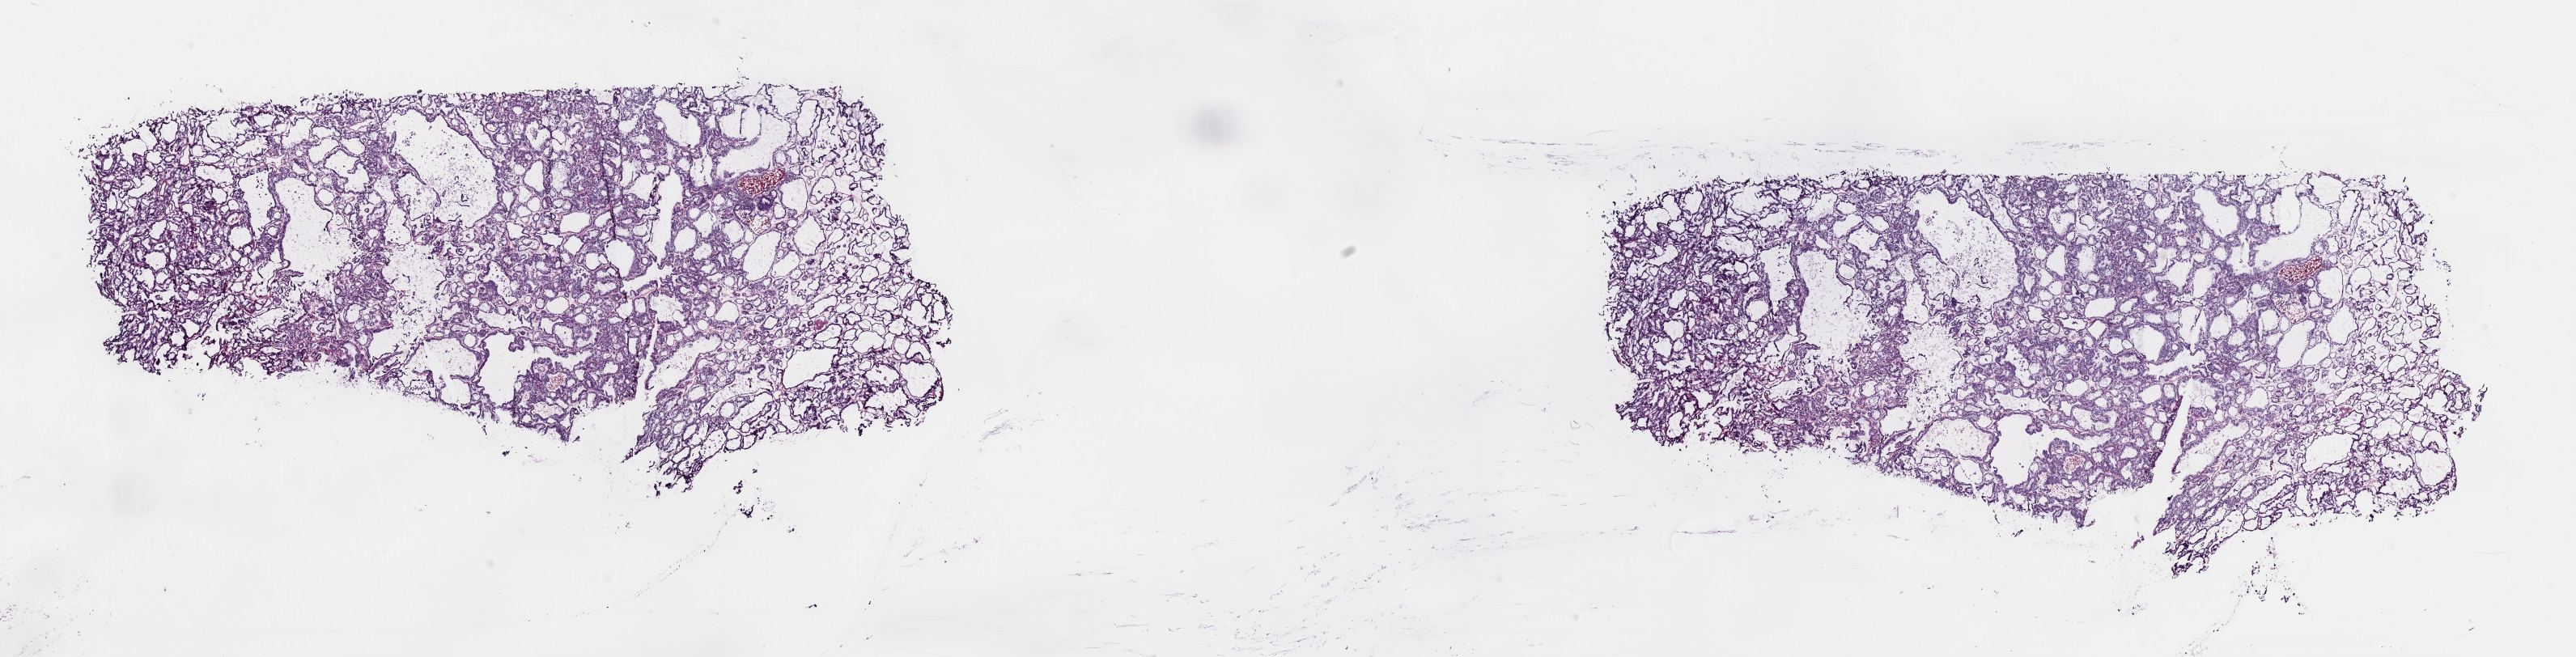
Whole-slide histology image, H&E — whole scanned area (about 25.1 x 6.4 mm, from a 40x scan) shown as a low-resolution overview. Frozen section. Primary tumour sample from the thyroid. Female patient; age at initial diagnosis 38 years. Composition of this section per pathologist review: tumour cells 75%, tumour nuclei 75%, normal cells 0%, stromal cells 21%, necrosis 4%. Inflammatory infiltration, as recorded: lymphocyte infiltration 4%, monocyte infiltration 1%, neutrophil infiltration 1%.
AJCC pathologic stage: I (7th edition). Pathologic diagnosis: Papillary carcinoma, follicular variant.